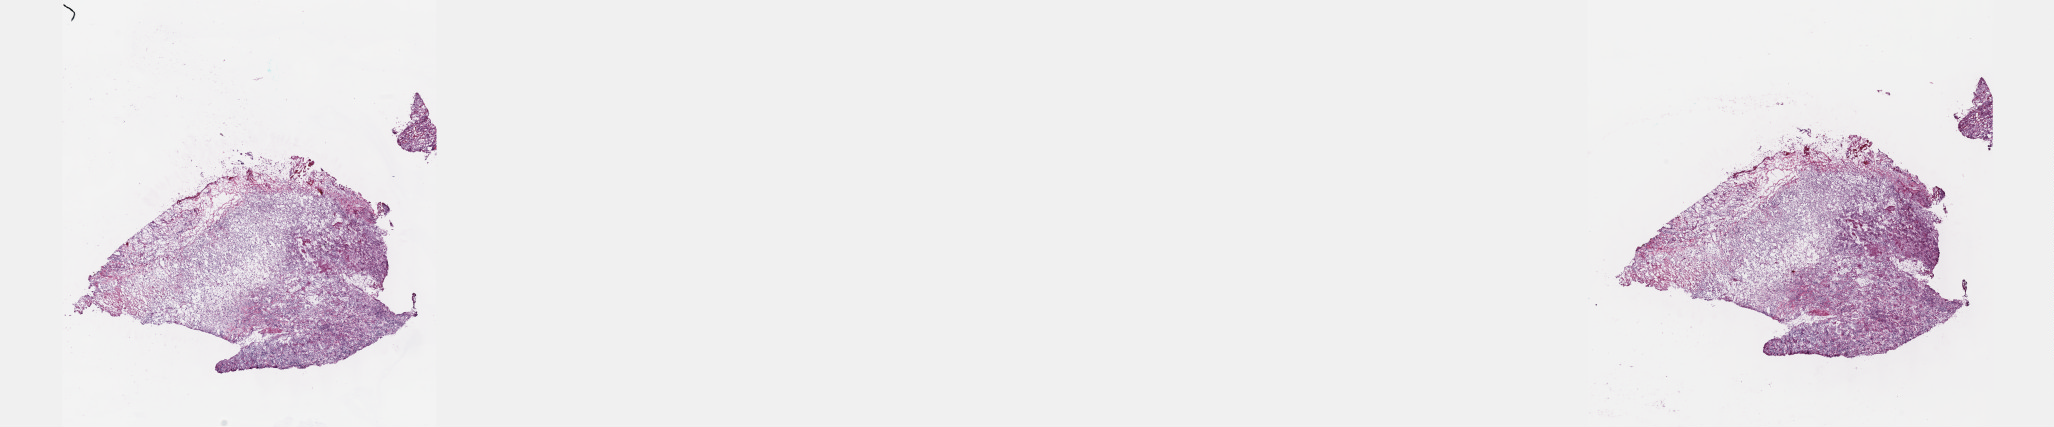
Whole-slide histology image, H&E — shown as a low-resolution overview of the whole scanned area (about 33.2 x 6.9 mm). Frozen section. Sample: primary tumour, adrenal gland. Female, age 35 years at initial diagnosis. Slide review estimates, as recorded: tumour cells 97%, tumour nuclei 80%, normal cells 0%, stromal cells 0%, necrosis 3%. Infiltration values recorded for this section: lymphocyte infiltration 1%, monocyte infiltration 0%, neutrophil infiltration 0%.
Histologic diagnosis: Pheochromocytoma, malignant.